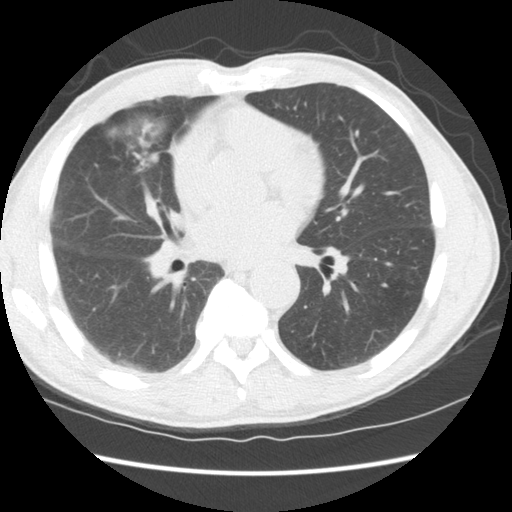
Axial slice from a low-dose chest CT screening exam; third screening round (two years after baseline); lung window (W 1500 / L -600 HU); 2.5 mm slice thickness; standard (soft-tissue) reconstruction kernel (STANDARD); slice 68 of 147 in the series. Male, age 65 years at enrolment. Current smoker at enrolment.
Expert-annotated lung lesion, box from (x=101, y=126) to (x=178, y=212) px. Reader record for this screening exam (exam-level; its link to the box is not recorded): non-calcified nodule or mass ≥4 mm, right middle lobe, 16 × 15 mm, smooth margins, soft tissue attenuation, pre-existing on the prior screen: yes; interval growth: yes.